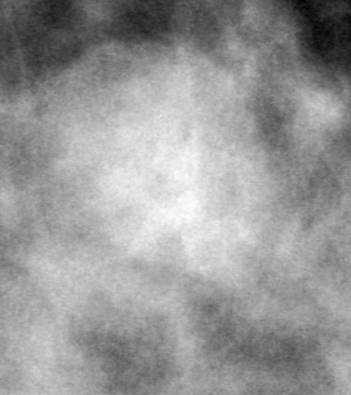
Region of interest cut from a scanned film mammogram (one marked finding), left breast, CC view, BI-RADS breast density category 2 (scale 1–4).
Finding: mass, shape oval, margins obscured; BI-RADS assessment category 0 (incomplete: needs additional imaging); subtlety rating 3 on a 1 (subtle) to 5 (obvious) scale; pathology (as recorded): benign.